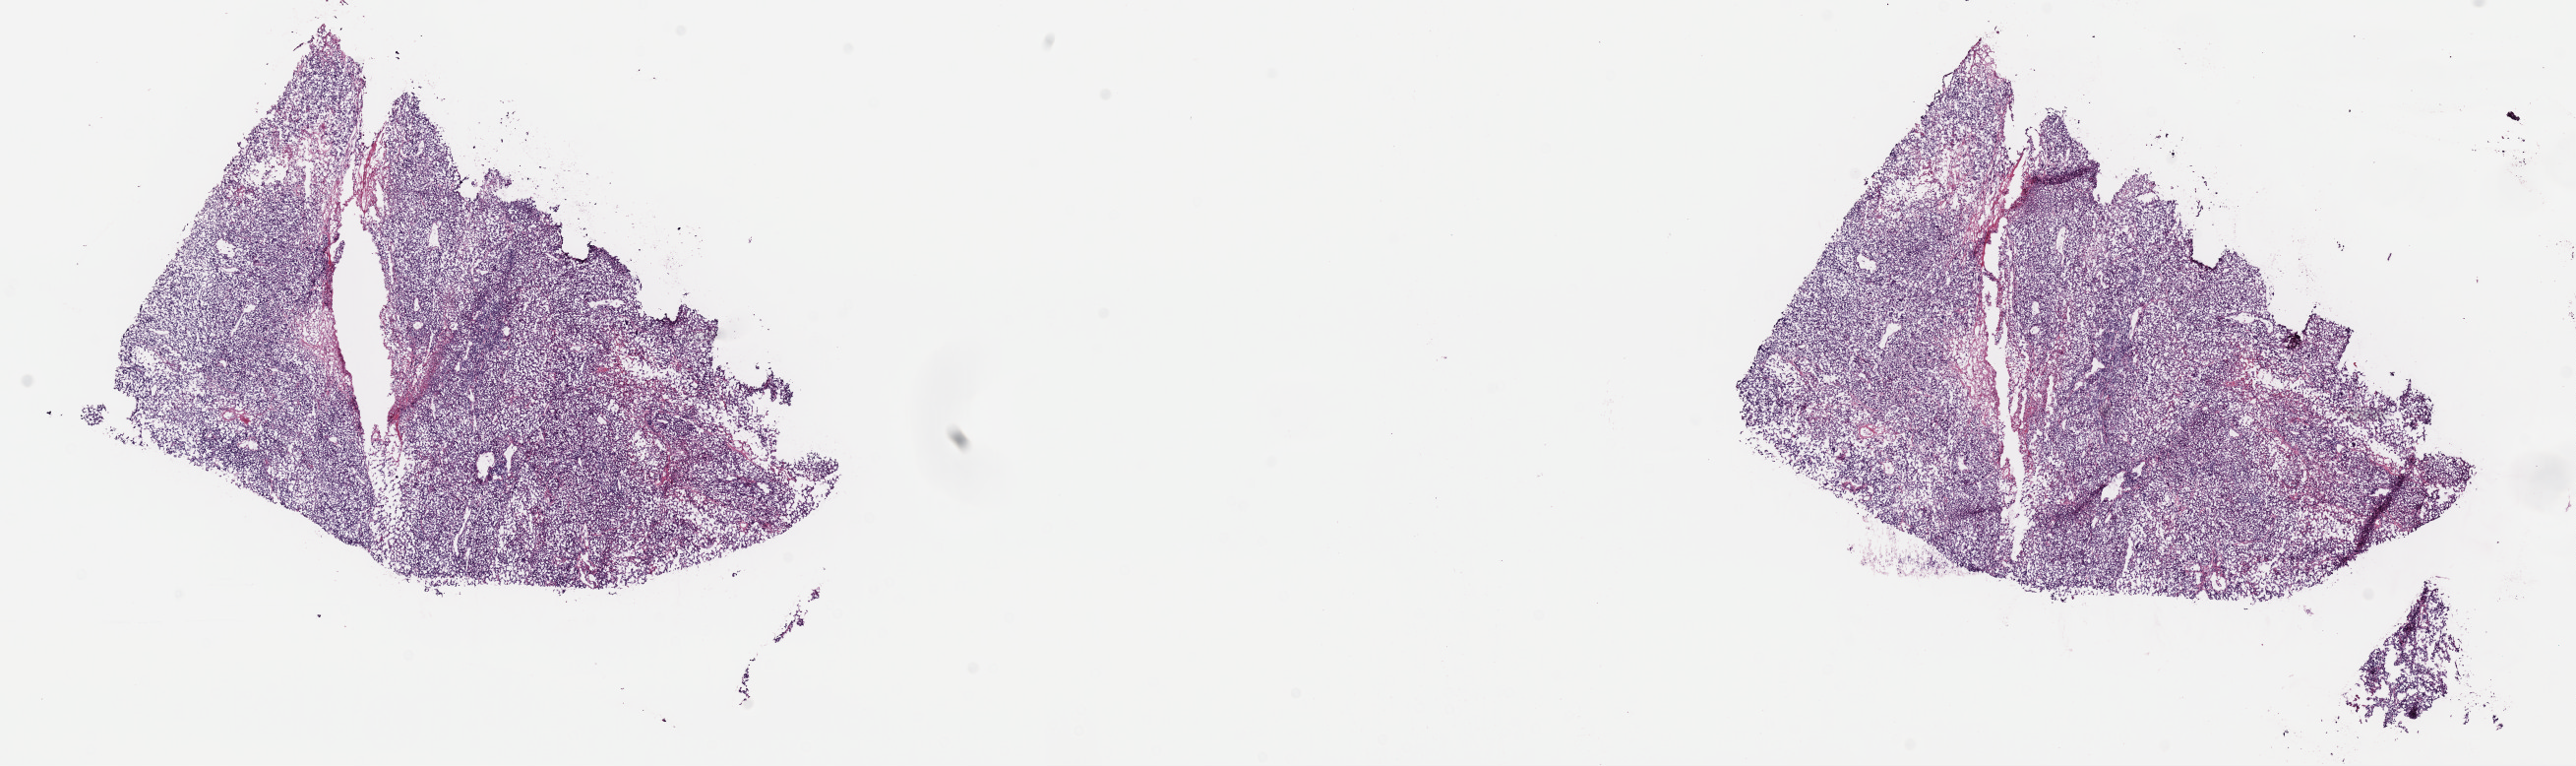
H&E-stained whole-slide image — low-resolution overview of the scanned area, about 20.7 x 6.1 mm. Frozen section from the top of the tissue portion. Metastatic tumour sample, sampled site: lymph nodes of axilla or arm. Male patient; age at initial diagnosis 45 years. Pathologist review of this section (percent, as recorded): tumour cells 75%, tumour nuclei 75%, normal cells 0%, stromal cells 15%, necrosis 10%. Infiltration values recorded for this section: lymphocyte infiltration 2%, monocyte infiltration 3%, neutrophil infiltration 0%.
This section: metastatic tumour tissue. Patient diagnosis: Malignant melanoma, NOS.